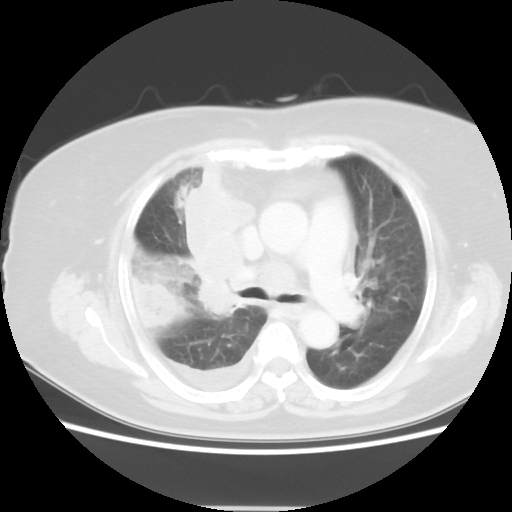
Chest CT, one axial slice. Position 31 of 48 along the scan axis. Reconstruction kernel STANDARD. 120 kVp. Lung window (W 1500 / L -600 HU). 5 mm slice thickness. 512 × 512 image matrix. Patient: female, 73 years. Case-level facts recorded for this patient, not image findings: clinical TNM (as recorded): T3 N3 M1b.
Outlined on this slice (rectangle marked by the reading radiologist):
- lung tumour (recorded histology: small cell carcinoma): bounding box [x1, y1, x2, y2] px = [185, 162, 263, 322]